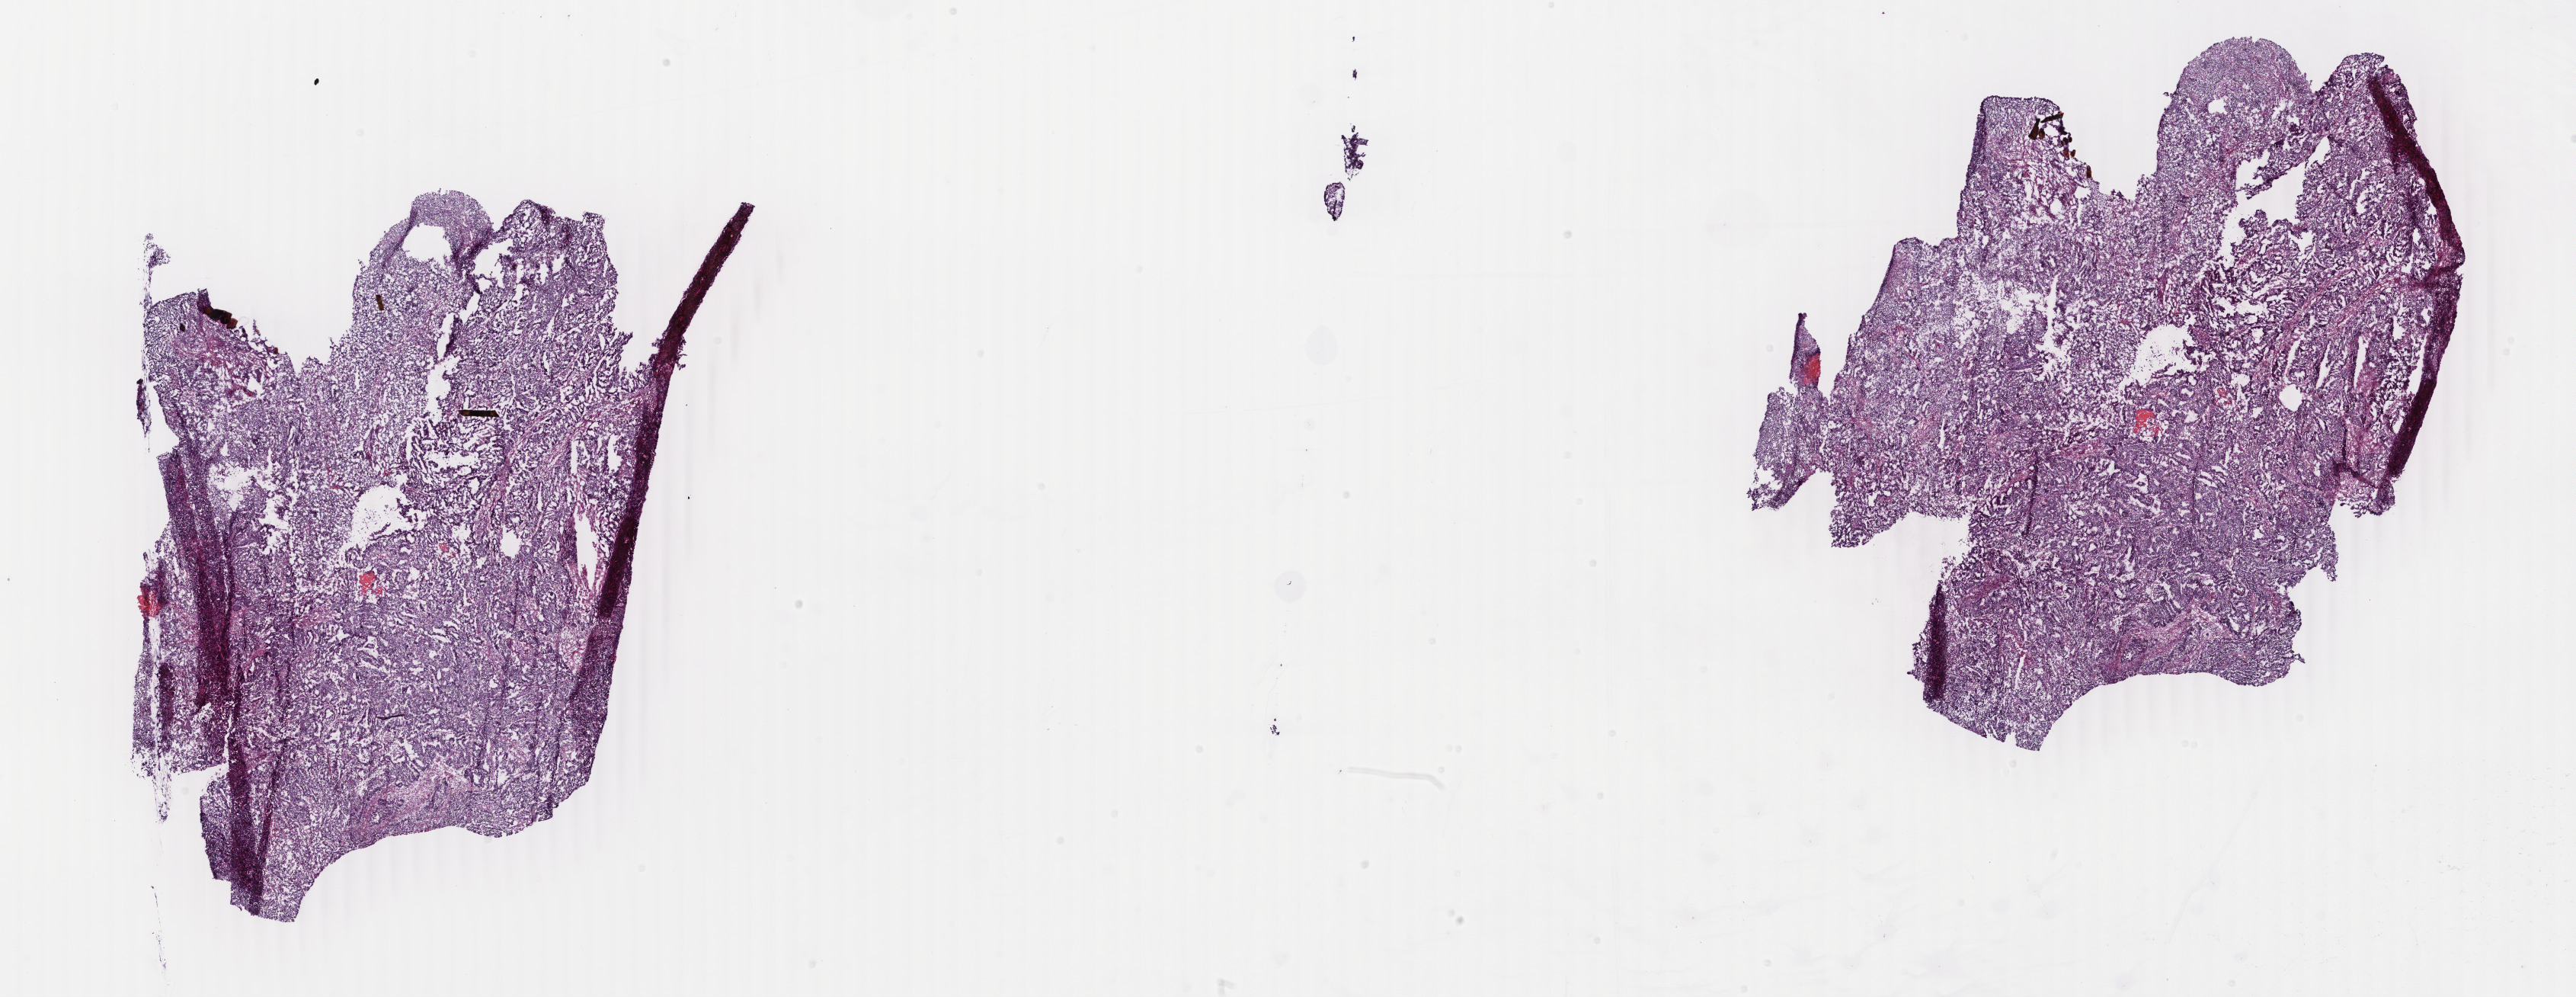
Hematoxylin and eosin (H&E) stained whole-slide image, shown as a low-resolution overview of the whole scanned area (about 26.9 x 10.4 mm, from a 40x scan), frozen section, primary tumour sample from the uterus. Female patient; age at initial diagnosis 53 years. Histologic grade: G1 (well differentiated). Pathologist review of this section (percent, as recorded): tumour cells 80%, tumour nuclei 85%, normal cells 11%, stromal cells 2%, necrosis 7%. Infiltration values recorded for this section: lymphocyte infiltration 1%, monocyte infiltration 0%, neutrophil infiltration 1%.
FIGO stage: IB. Pathologic diagnosis: Endometrioid adenocarcinoma, NOS. Lymph nodes positive (case pathology): 0 of 8 examined.